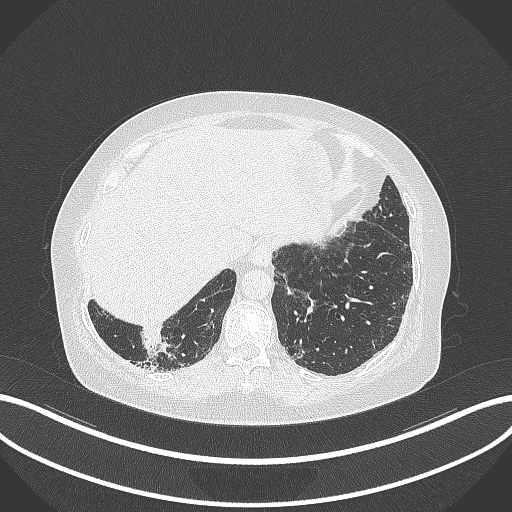
Chest CT, one axial slice; slice 19 of 296 in the series (ordered by position); 120 kVp; lung window (W 1500 / L -600 HU); 512 × 512 image matrix, field of view 400 × 400 mm. Female patient, age 65 years. From the clinical record (not read from this slice): clinical TNM (as recorded): T2b N1 M0; histopathological grade: G1.
Outlined on this slice (rectangle marked by the reading radiologist):
- lung tumour (recorded histology: adenocarcinoma): bounding box [x1, y1, x2, y2] px = [139, 326, 171, 361]